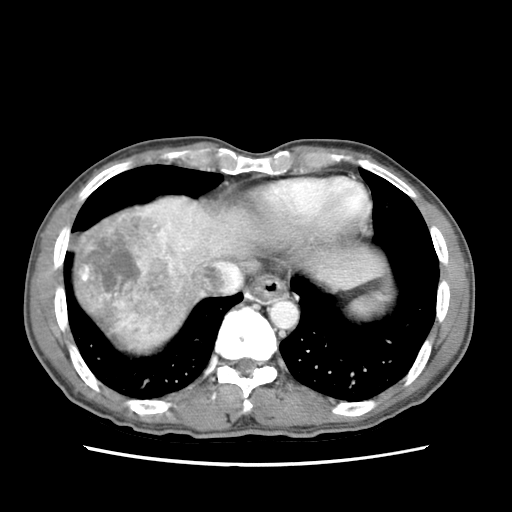
Contrast-enhanced abdominal CT (liver protocol), one axial slice. Position 66 of 79 along the scan axis. Reconstruction kernel STANDARD. 120 kVp. Soft-tissue window (W 400 / L 40 HU). 2.5 mm slice thickness. 512 × 512 image matrix, field of view 320 × 320 mm. From the clinical record (not read from this slice): diagnosis: hepatocellular carcinoma (patient treated with transarterial chemoembolisation; whether this scan precedes or follows treatment is not stated here); TNM stage (as recorded): Stage-IIIB.
Structures marked on this image (semi-automatic segmentation, software-assisted and operator-edited):
- abdominal aorta: bounding box (x1, y1, x2, y2) in pixels: (272, 301, 296, 327)
- liver parenchyma outside the tumour (the mass and vessels are separate outlines, so this box may not span the whole liver): (71, 194, 306, 356)
- mass: (71, 194, 197, 331)
- liver vessels: (196, 248, 219, 271)